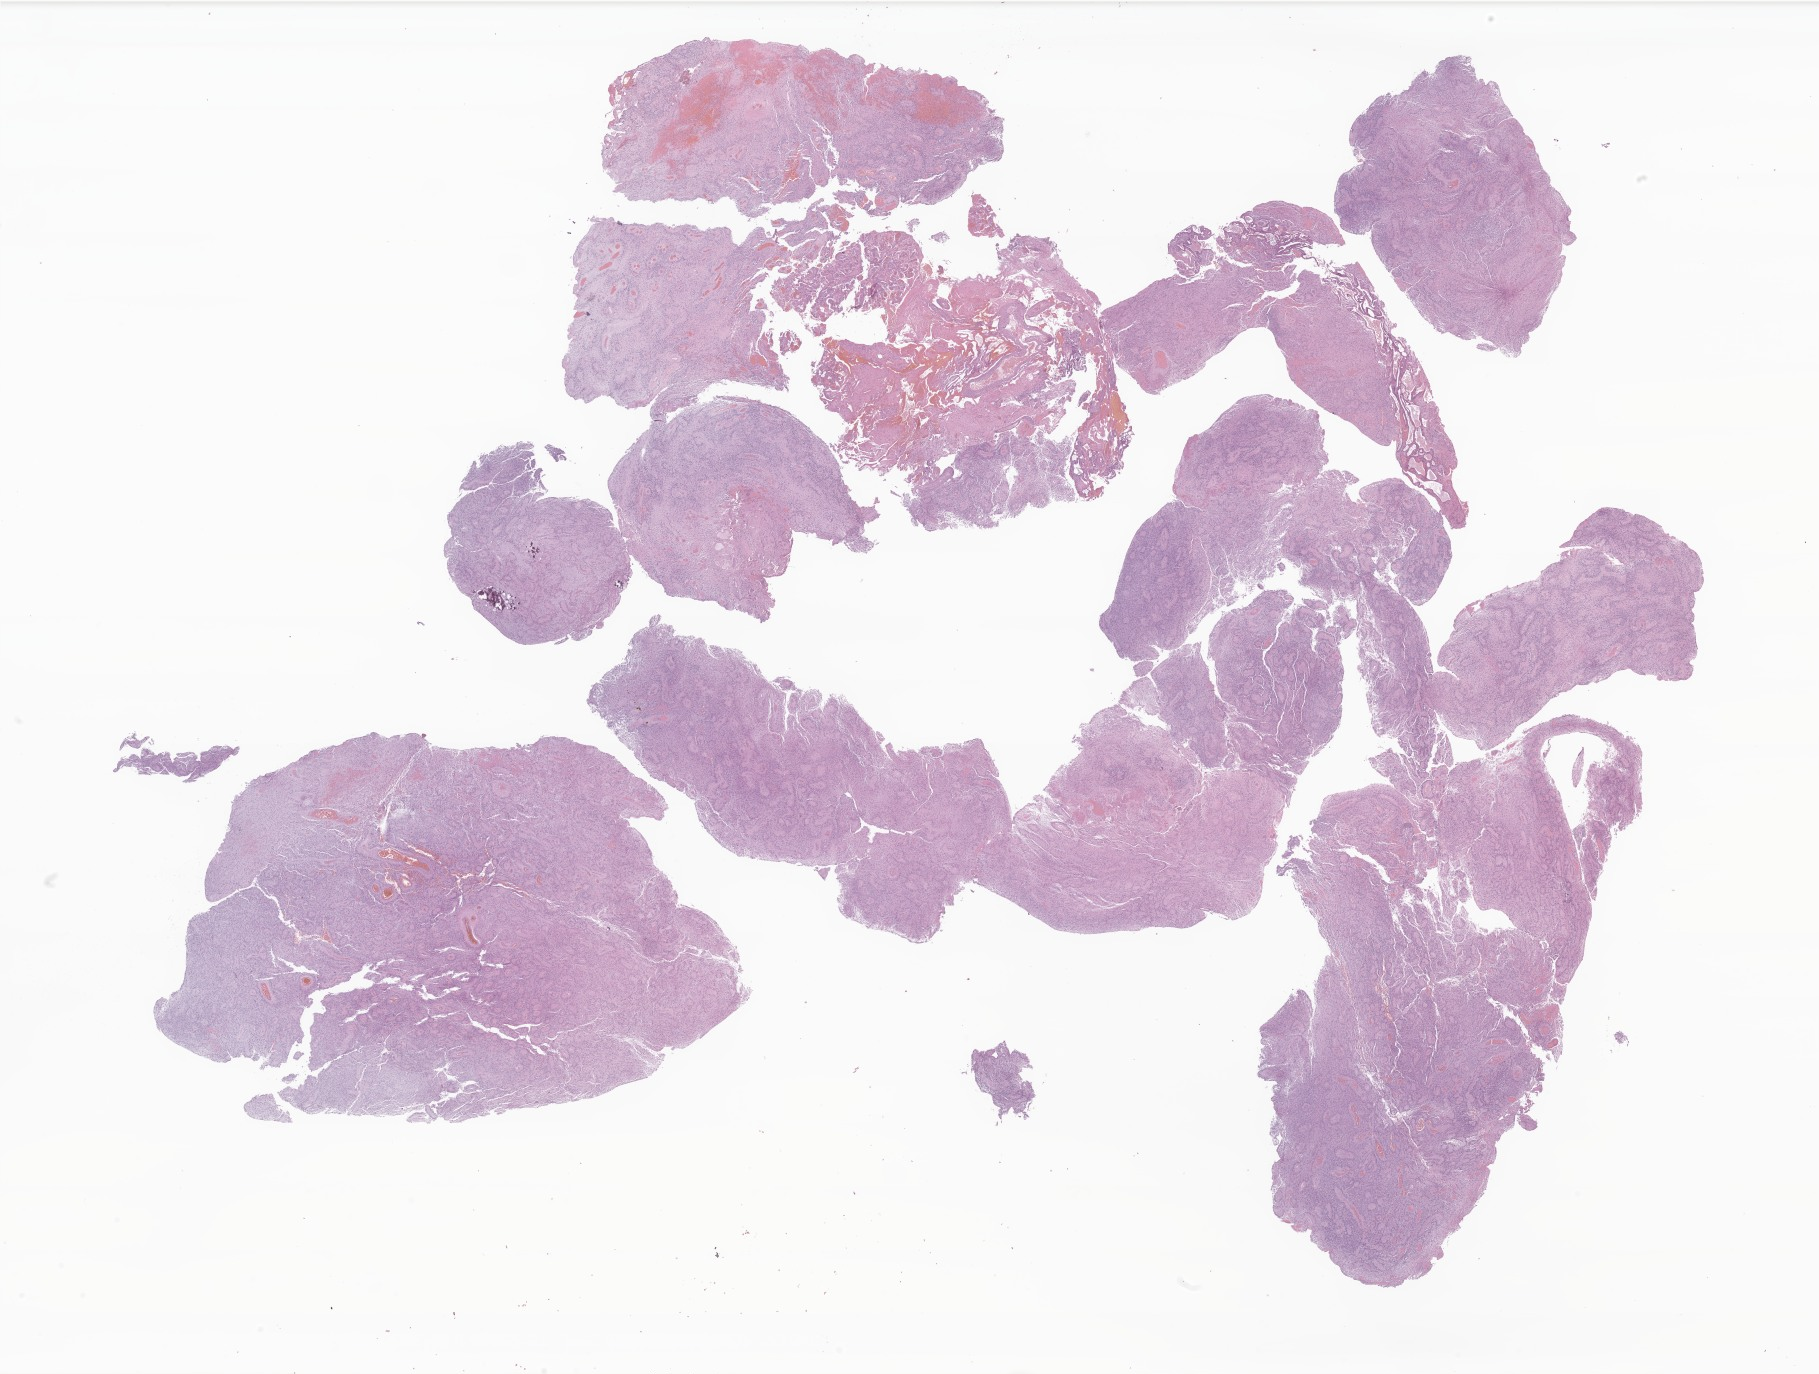
Digitized hematoxylin and eosin (H&E)-stained section of tumor tissue from the brain stem — a low-resolution overview of the entire scanned area, about 30.7 x 23.2 mm; FFPE section. Patient female; age 154 months (12 years 10 months).
- diagnosis (ICD-O-3 morphology term): Ependymoma, NOS